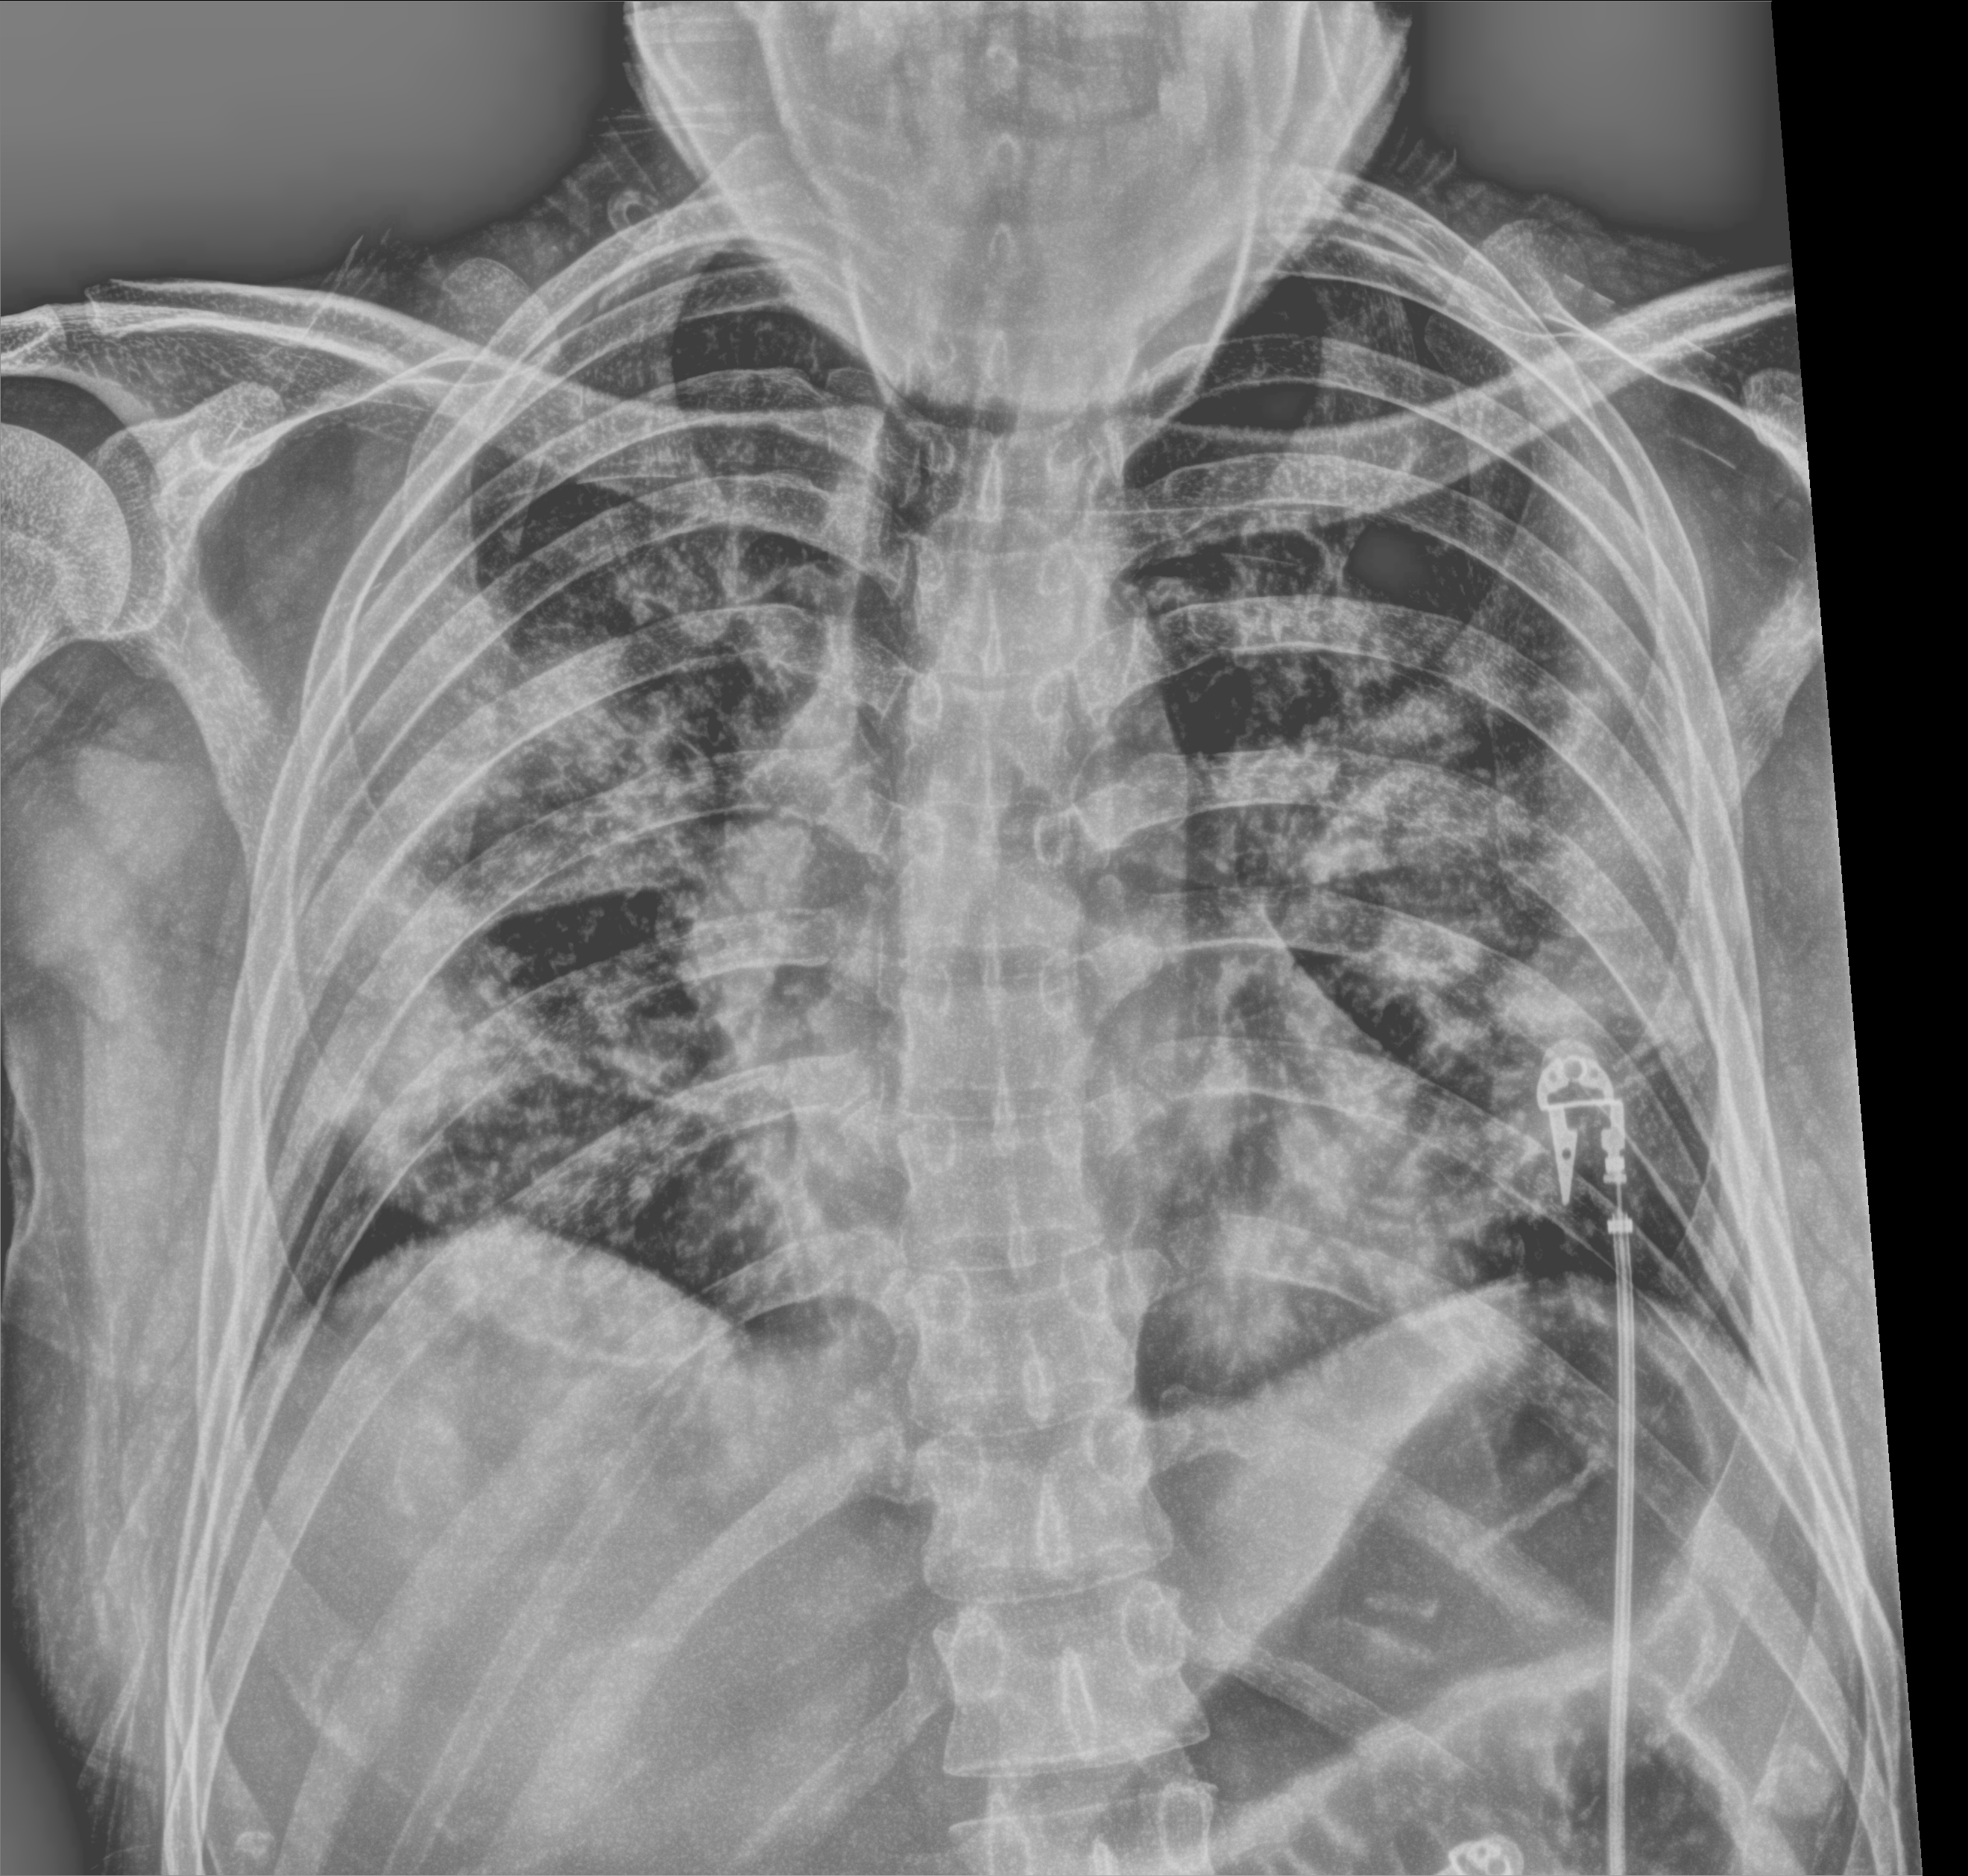
Portable chest radiograph; anteroposterior (AP) projection. Patient hospitalised with COVID-19; male, aged 18–59 years.
Hospital-stay facts (about this admission, not read from this image; timing relative to this image not recorded): diabetes (admission record): no; hypertension (admission record): no; length of hospital stay: 12 days.